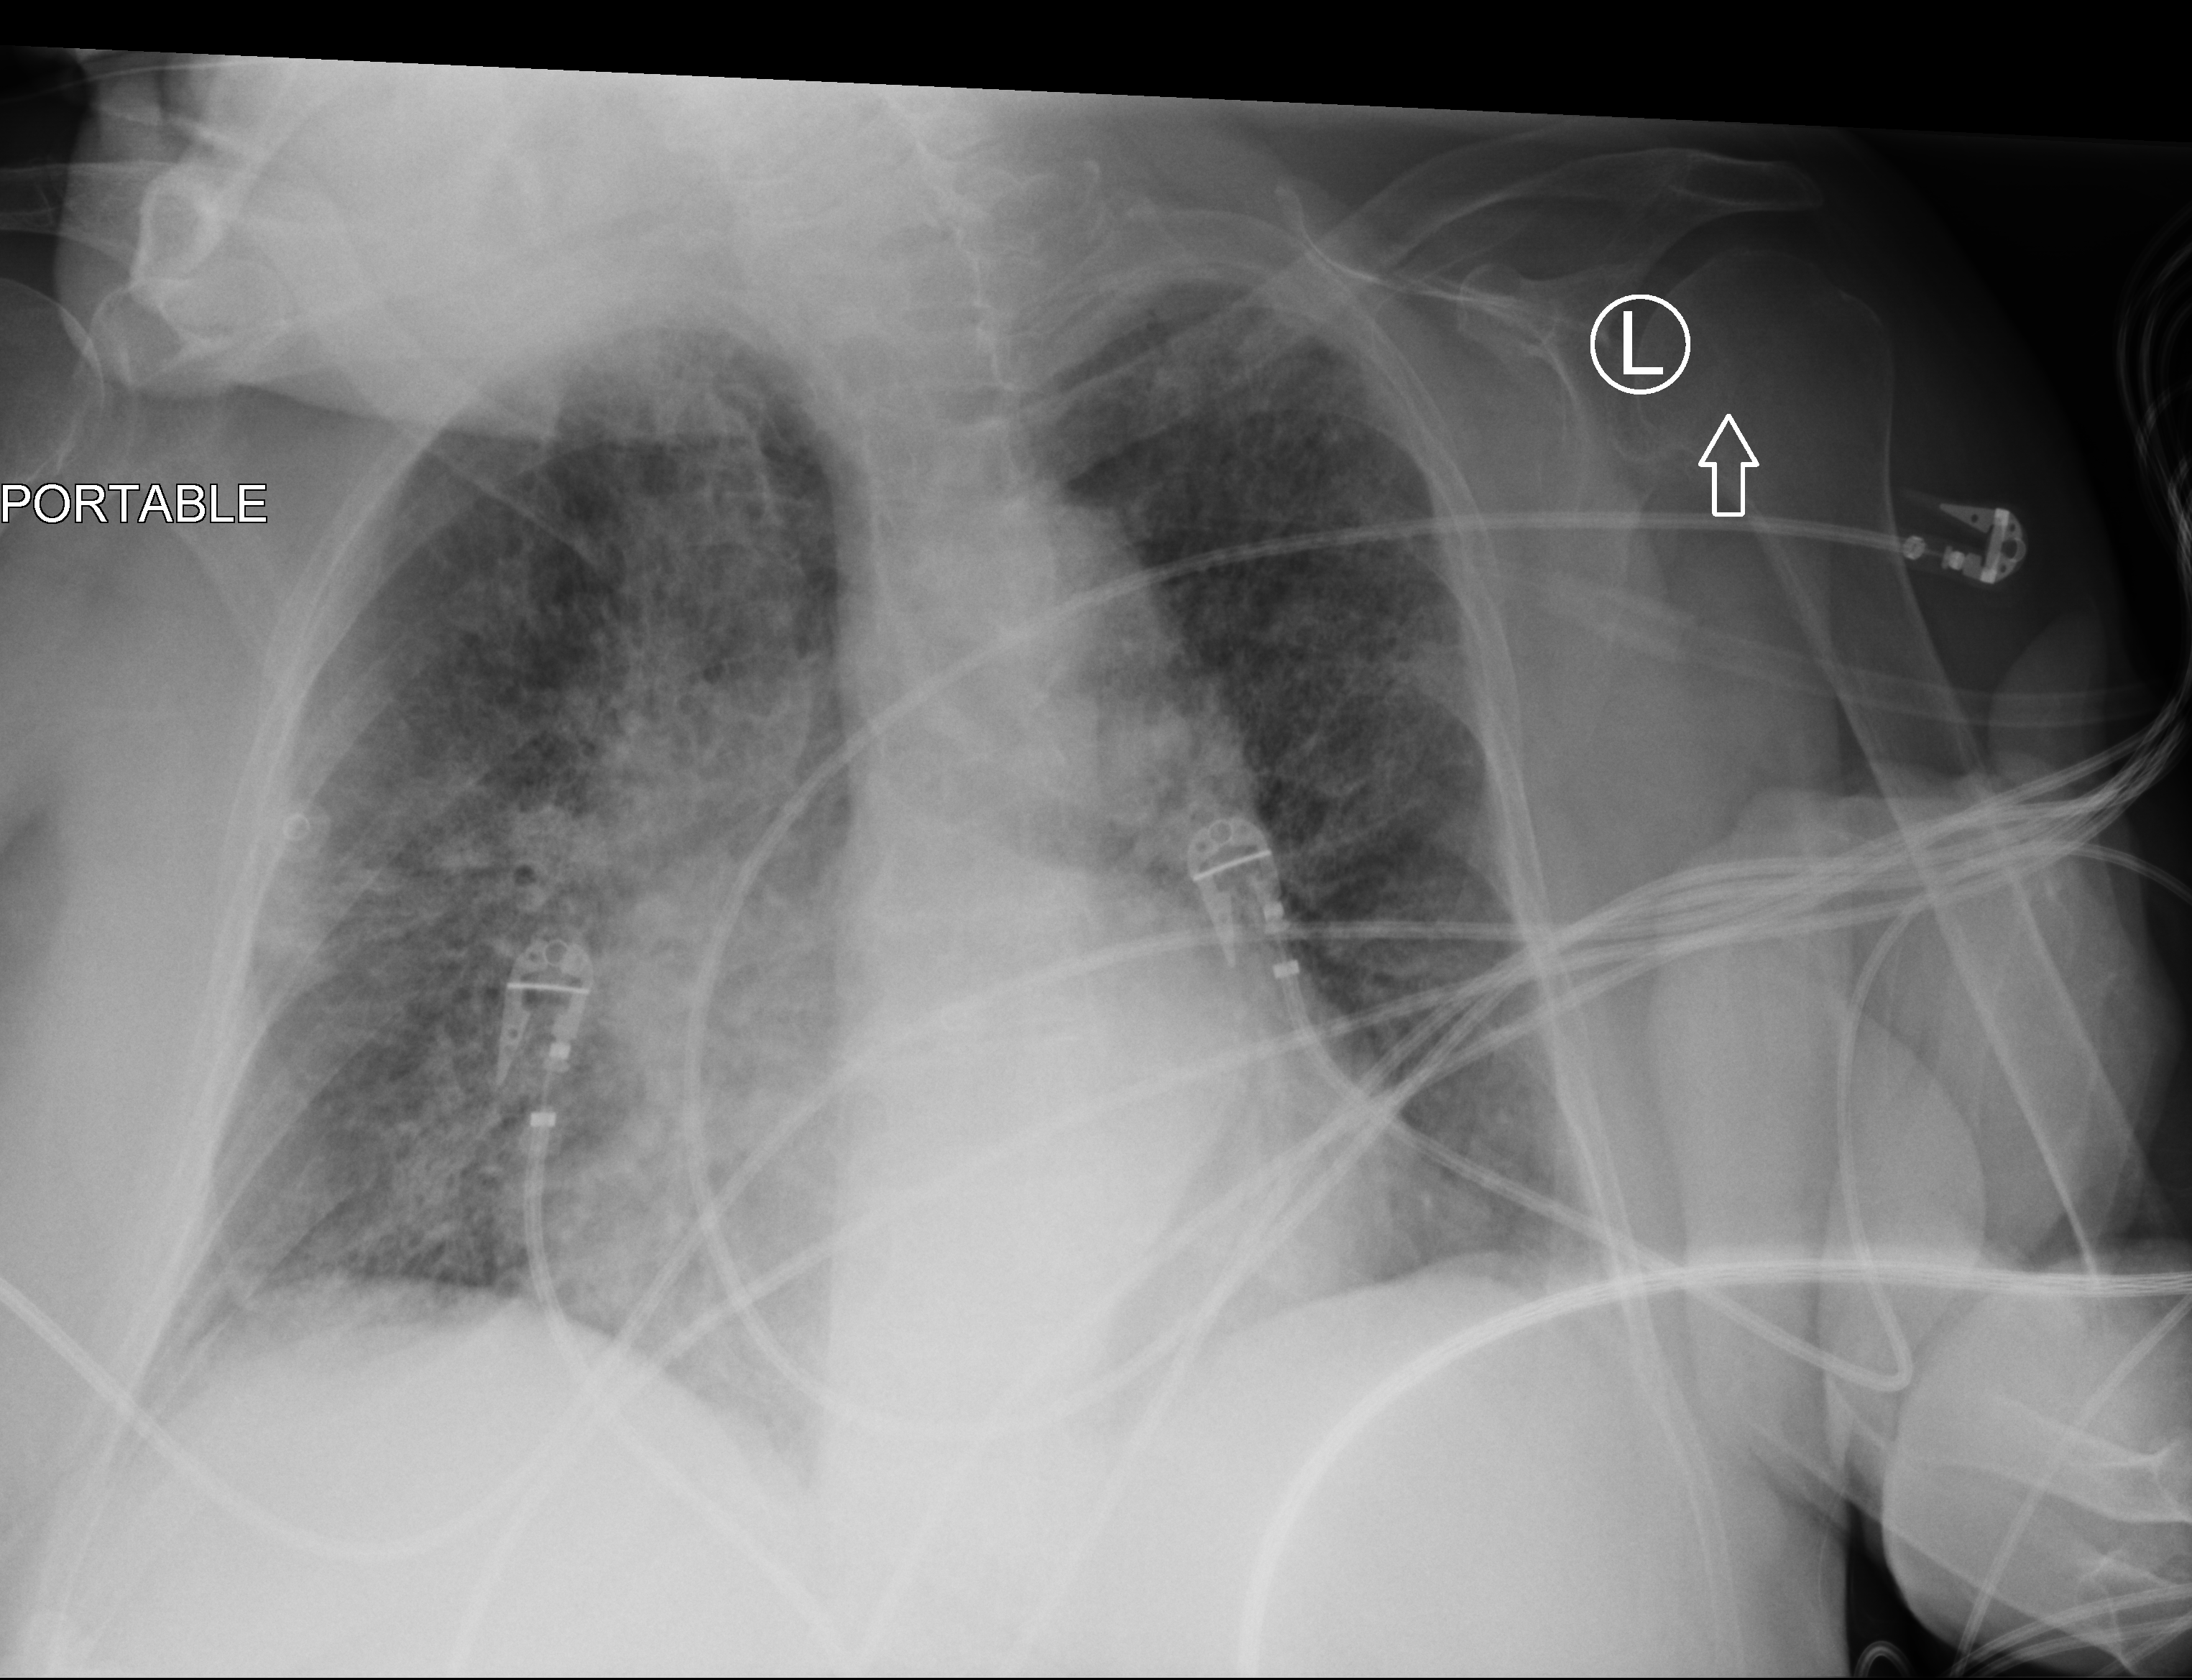
Chest X-ray (portable); anteroposterior (AP) projection. Patient hospitalised with COVID-19; female, aged 75–90 years.
From the hospital-stay record, not from the radiograph (when in the stay this image was taken is not recorded):
- admitted to intensive care during this hospital stay: no
- COPD (admission record): yes